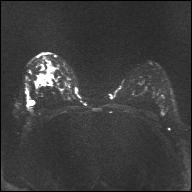
Breast MRI, one axial slice. Position 21 of 32 along the scan axis. Diffusion-weighted series; image 2 of 4 stored at this slice position (different b-values; order by instance number). 1.5 T. 4 mm slice thickness. 192 × 192 image matrix, field of view 360 × 360 mm. Female patient.
Annotated regions visible in this slice (manually delineated by an expert):
- tumour on diffusion-weighted imaging: bounding box [x1, y1, x2, y2] px = [39, 74, 52, 82]